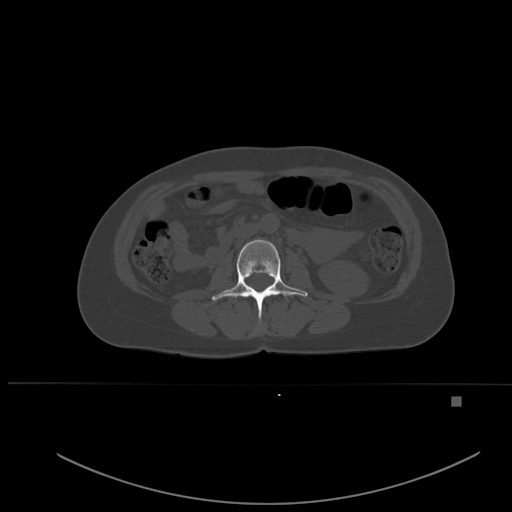
CT including the spine, one axial slice; slice 213 of 651 in the series (ordered by position); bone window (W 1800 / L 400 HU); 512 × 512 image matrix, field of view 443 × 443 mm. Patient: female, 49 years. From the clinical record (not read from this slice): primary cancer: breast; vertebrae with lytic lesions (as recorded): L3, T12, L4.
Annotated regions visible in this slice (semi-automatic segmentation, software-assisted and operator-edited):
- L2 vertebra: box from (x=212, y=239) to (x=308, y=320) px